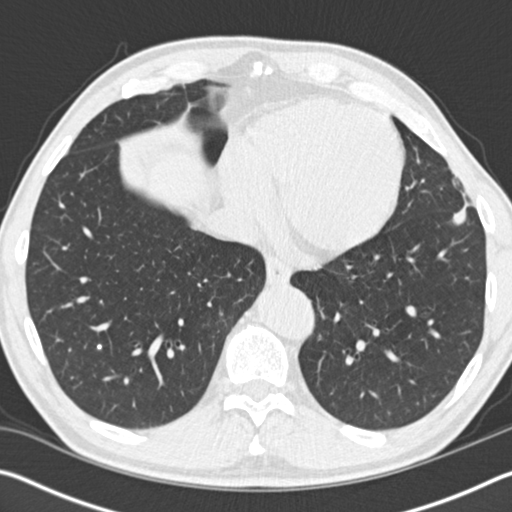
Low-dose screening chest CT, one axial slice; slice 44 of 162 in the series (ordered by position); lung window (W 1500 / L -600 HU); 512 × 512 image matrix, field of view 340 × 340 mm.
Outlined on this slice (outlined manually by an expert reader):
- lesion 1 (tumor, upper lobe of left lung): bounding box [x1, y1, x2, y2] px = [452, 177, 472, 225]